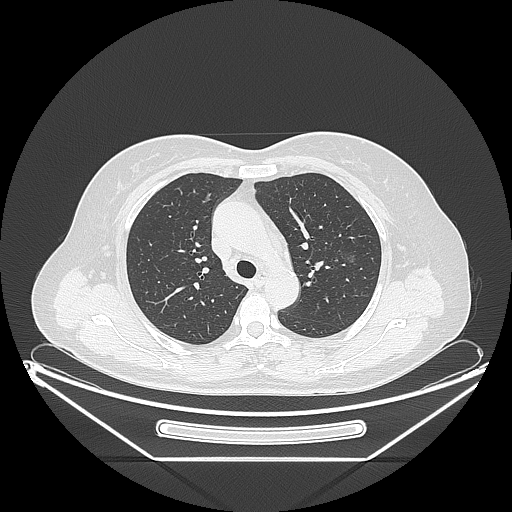
Chest CT, one axial slice; slice 150 of 226 in the series (ordered by position); reconstruction kernel LUNG; 120 kVp; lung window (W 1500 / L -600 HU); 1.25 mm slice thickness; 512 × 512 image matrix, field of view 447 × 447 mm. Patient: female, 54 years. Case-level facts recorded for this patient, not image findings: clinical TNM (as recorded): T1c N0 M0.
Structures marked on this image (bounding box drawn by a radiologist):
- lung tumour (recorded histology: adenocarcinoma): bounding box (x1, y1, x2, y2) in pixels: (328, 248, 361, 274)